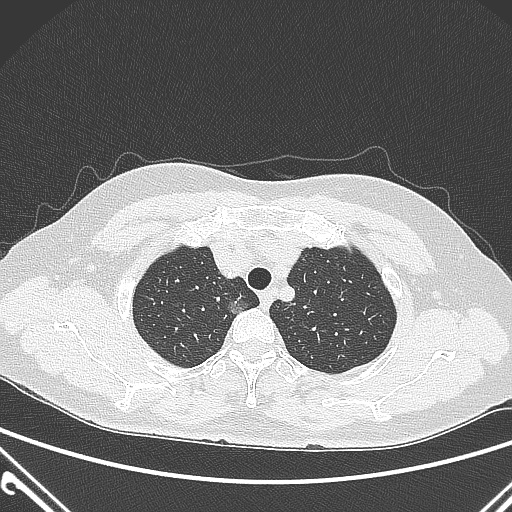
Chest CT, one axial slice; position 239 of 300 along the scan axis; 120 kVp; lung window (W 1500 / L -600 HU); 1 mm slice thickness; 512 × 512 image matrix, field of view 350 × 350 mm. Female patient, age 54 years. Case-level facts recorded for this patient, not image findings: clinical TNM (as recorded): T1a N0 M0.
Outlined on this slice (rectangle marked by the reading radiologist):
- lung tumour (recorded histology: adenocarcinoma): bounding box (x1, y1, x2, y2) in pixels: (227, 292, 250, 320)